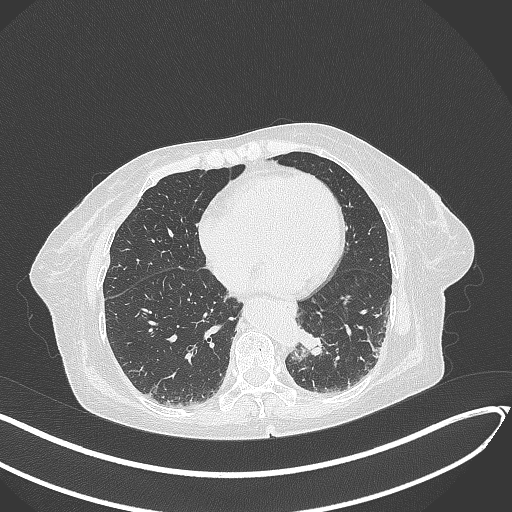
Chest CT, one axial slice. Position 71 of 324 along the scan axis. Reconstruction kernel B70f. 120 kVp. Lung window (W 1500 / L -600 HU). 512 × 512 image matrix. Female patient, age 82 years. Case-level facts recorded for this patient, not image findings: clinical TNM (as recorded): T1b N0 M1.
Structures marked on this image (bounding box drawn by a radiologist):
- lung tumour (recorded histology: adenocarcinoma): bounding box [x1, y1, x2, y2] px = [296, 325, 329, 364]